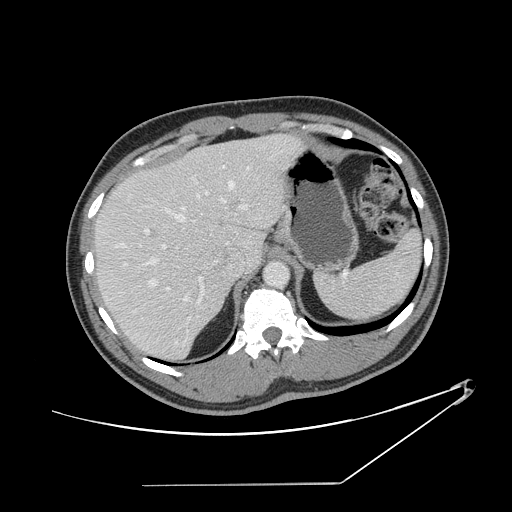
Contrast-enhanced abdominal CT, one axial slice; position 106 of 152 along the scan axis; 120 kVp; soft-tissue window (W 400 / L 40 HU); 2.5 mm slice thickness; 512 × 512 image matrix. Male patient, age 45 years. From the clinical record (not read from this slice): diagnosis: colorectal cancer liver metastases, imaged before liver resection; multiple liver metastases: no; largest metastasis: 1 cm; chemotherapy before resection: yes.
Outlined on this slice (outlined manually by an expert reader):
- hepatic veins: bounding box [x1, y1, x2, y2] px = [111, 166, 250, 302]
- liver: [96, 135, 298, 361]
- planned liver remnant (the part of the liver to remain after resection): [96, 154, 234, 361]
- portal vein (with intrahepatic branches): [162, 192, 248, 325]